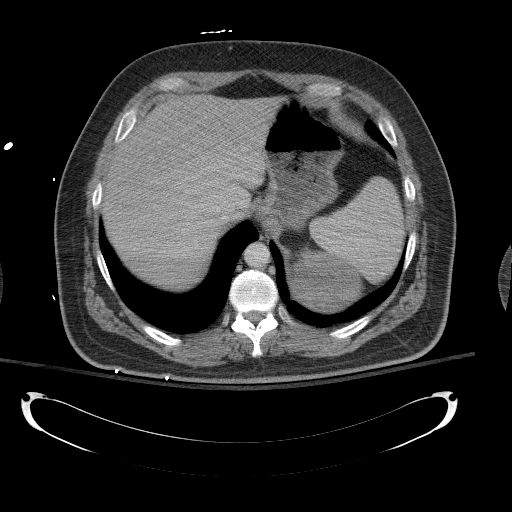
Contrast-enhanced abdominal CT, one axial slice; slice 98 of 154 in the series (ordered by position); intravenous contrast given; soft-tissue window (W 400 / L 40 HU); 5 mm slice thickness; 512 × 512 image matrix. Patient: male, 43 years. From the clinical record (not read from this slice): diagnosis: adrenocortical carcinoma; tumour side: left adrenal; tumour size at pathology: 9.8 cm; Ki-67 index: 30 %; stage (as recorded): 2.
Structures marked on this image (semi-automatically segmented with operator editing):
- mass: bounding box (x1, y1, x2, y2) in pixels: (292, 248, 360, 311)